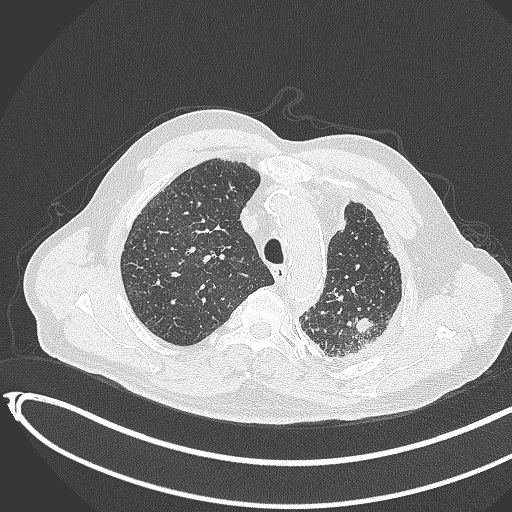
Chest CT, one axial slice. Slice 336 of 451 in the series (ordered by position). Reconstruction kernel B70f. 120 kVp. Lung window (W 1500 / L -600 HU). 512 × 512 image matrix. Patient: male, 78 years. From the clinical record (not read from this slice): clinical TNM (as recorded): T1c N0 M1.
Structures marked on this image (bounding box drawn by a radiologist):
- lung tumour (recorded histology: adenocarcinoma): box from (x=355, y=309) to (x=380, y=343) px